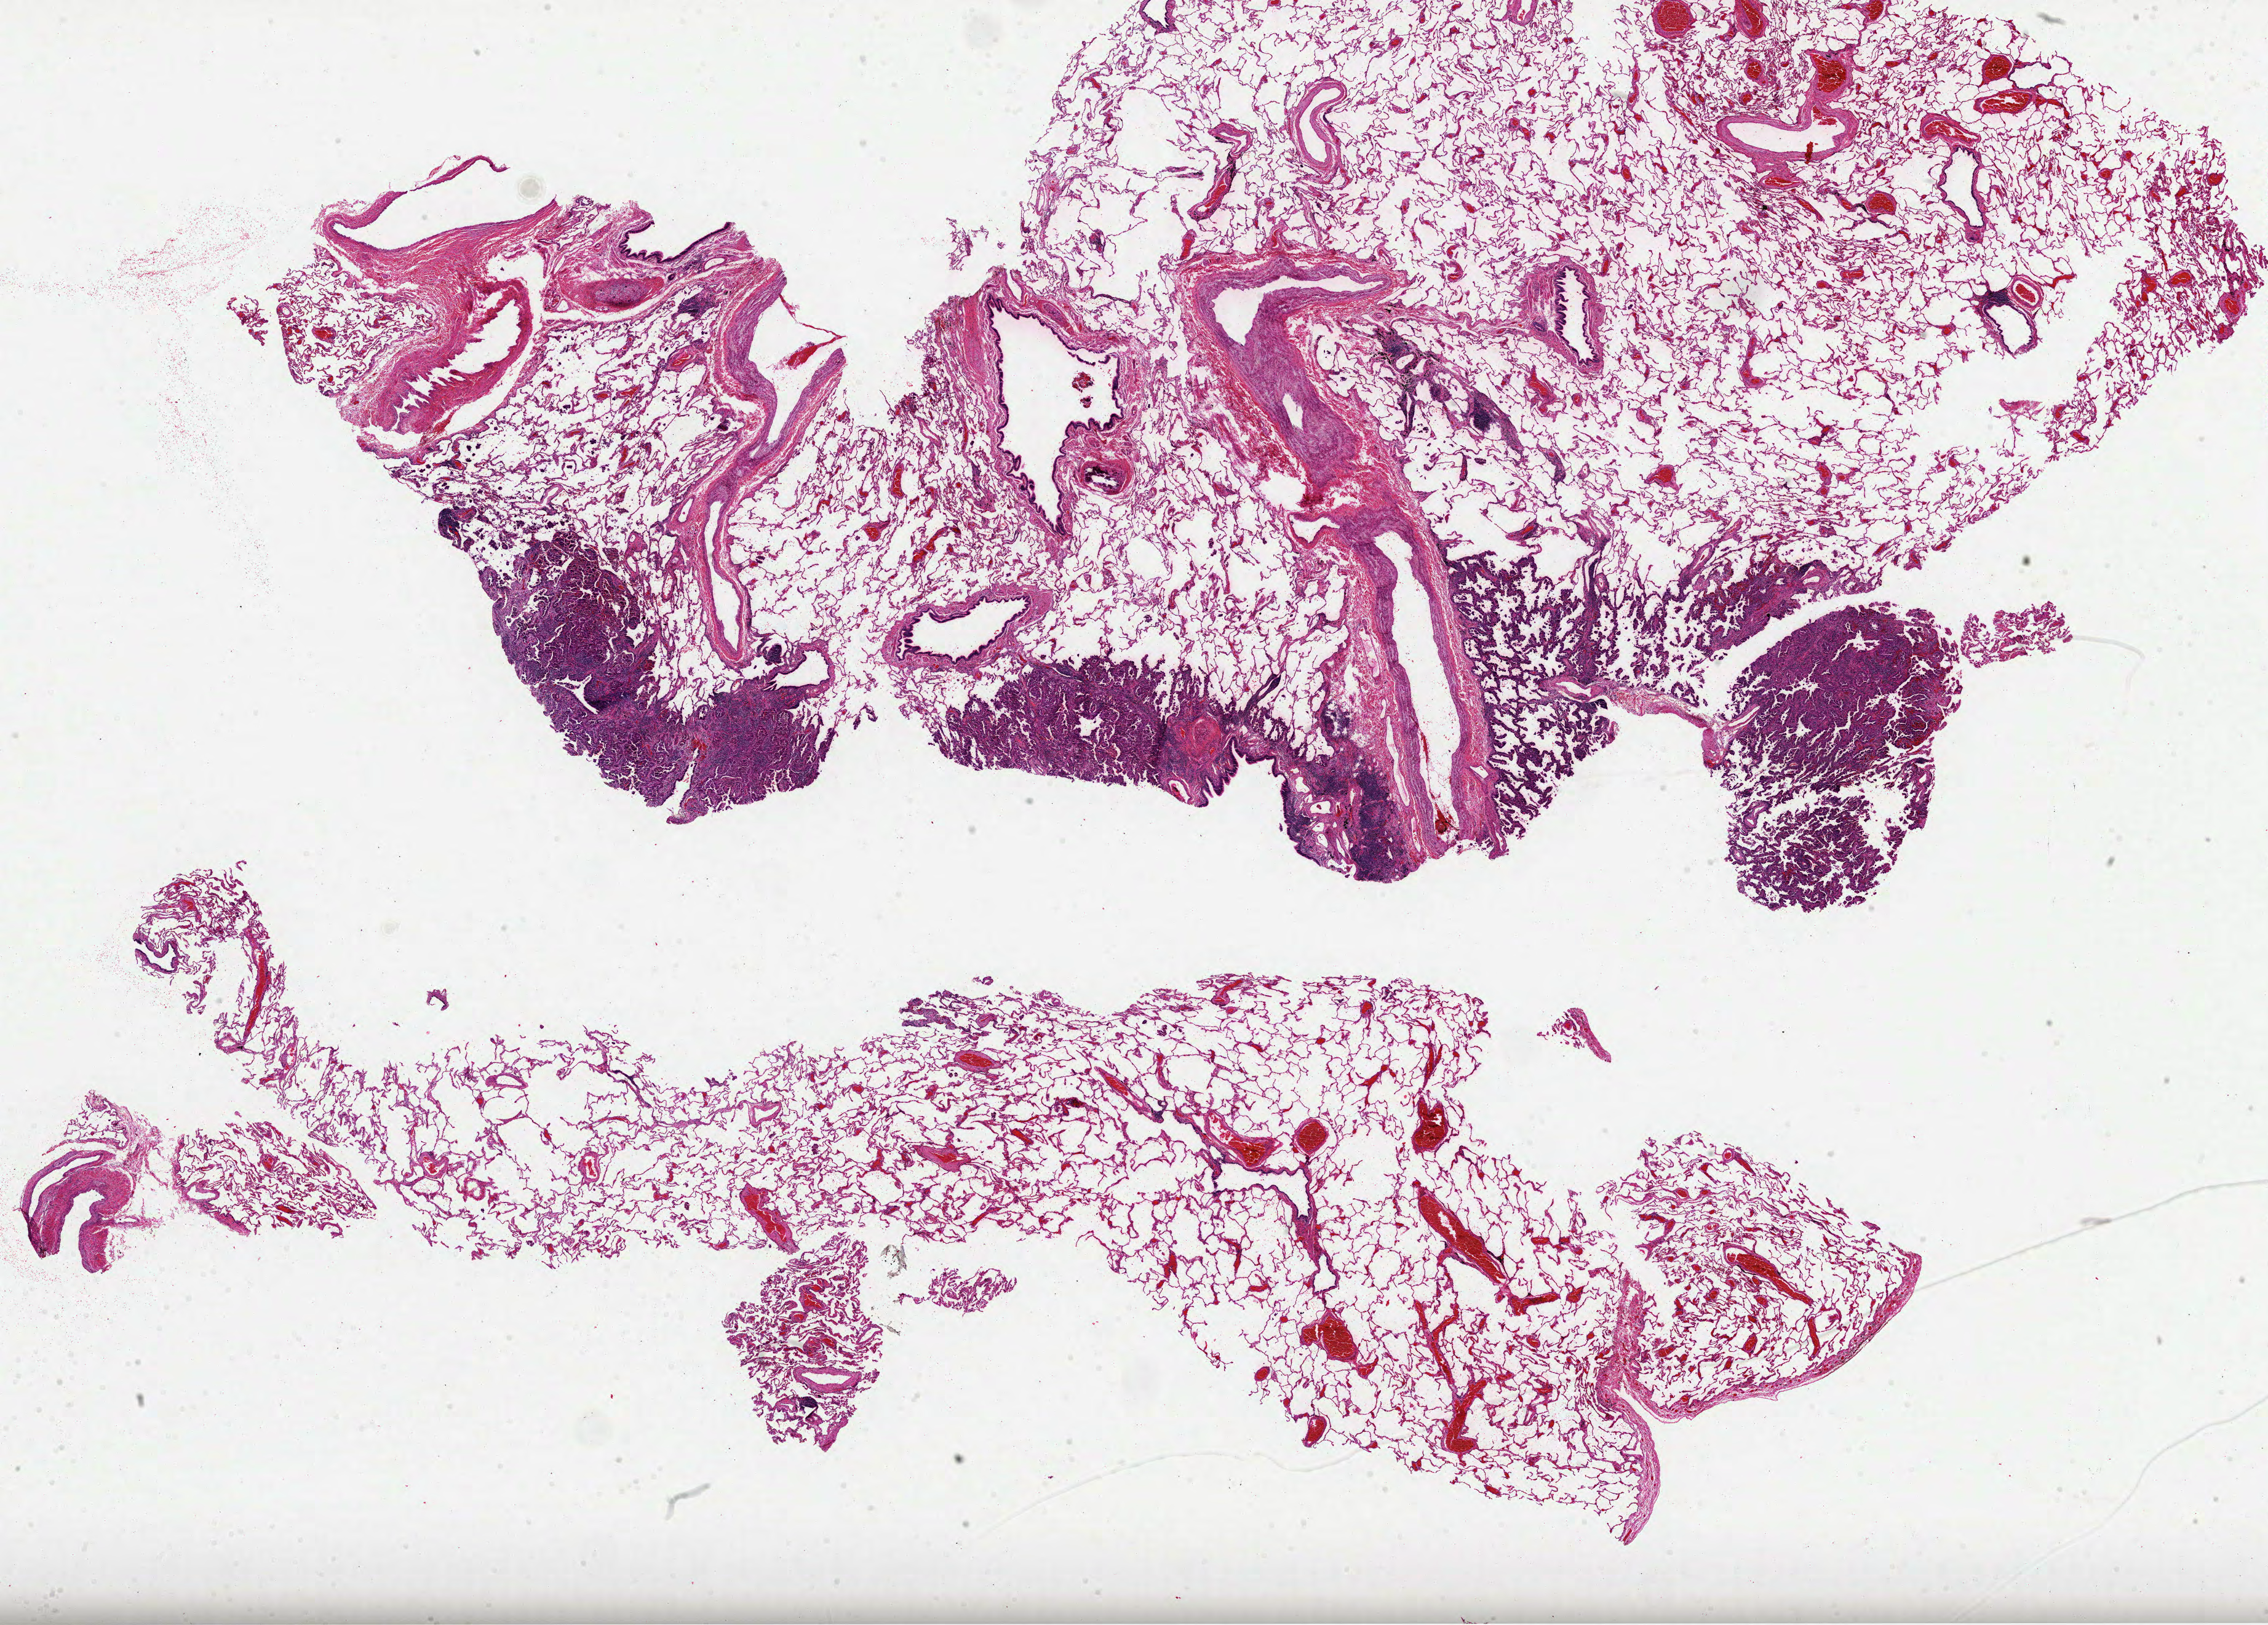
Digitized Hematoxylin and eosin (H&E) stained tissue section (whole slide), a low-resolution overview of the entire scanned area, about 29.7 x 21.3 mm (slide scanned at 40x), FFPE section, lung, primary tumour sample. Female patient; age at initial diagnosis 74 years.
Diagnosis: Adenocarcinoma, NOS.